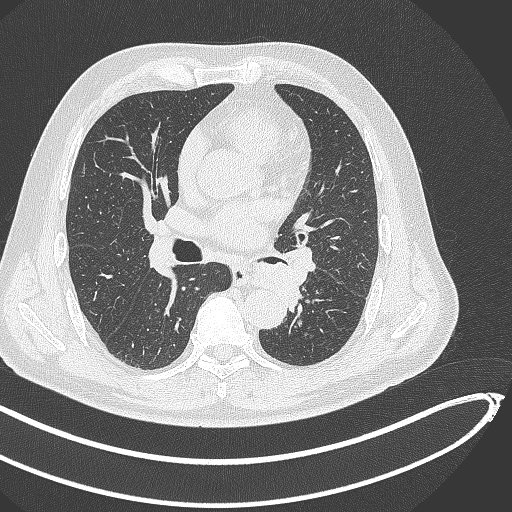
Chest CT, one axial slice; slice 253 of 468 in the series (ordered by position); 120 kVp; lung window (W 1500 / L -600 HU); 1 mm slice thickness; 512 × 512 image matrix. Patient: male, 64 years. Case-level facts recorded for this patient, not image findings: clinical TNM (as recorded): T1c N0 M0; histopathological grade: G2.
Outlined on this slice (bounding box drawn by a radiologist):
- lung tumour (recorded histology: squamous cell carcinoma): bounding box [x1, y1, x2, y2] px = [255, 261, 308, 311]